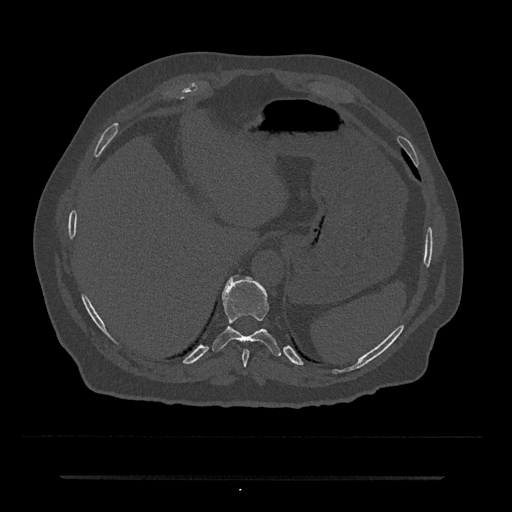
CT including the spine, one axial slice; position 234 of 797 along the scan axis; reconstruction kernel Br40s/3; bone window (W 1800 / L 400 HU); 0.5 mm slice thickness; 512 × 512 image matrix. Patient: male, 69 years. Case-level facts recorded for this patient, not image findings: primary cancer: prostate.
Annotated regions visible in this slice (semi-automatic segmentation, software-assisted and operator-edited):
- T10 vertebra: bounding box <212,275,281,356> (left, top, right, bottom; pixels)
- T9 vertebra: <242,349,249,366>